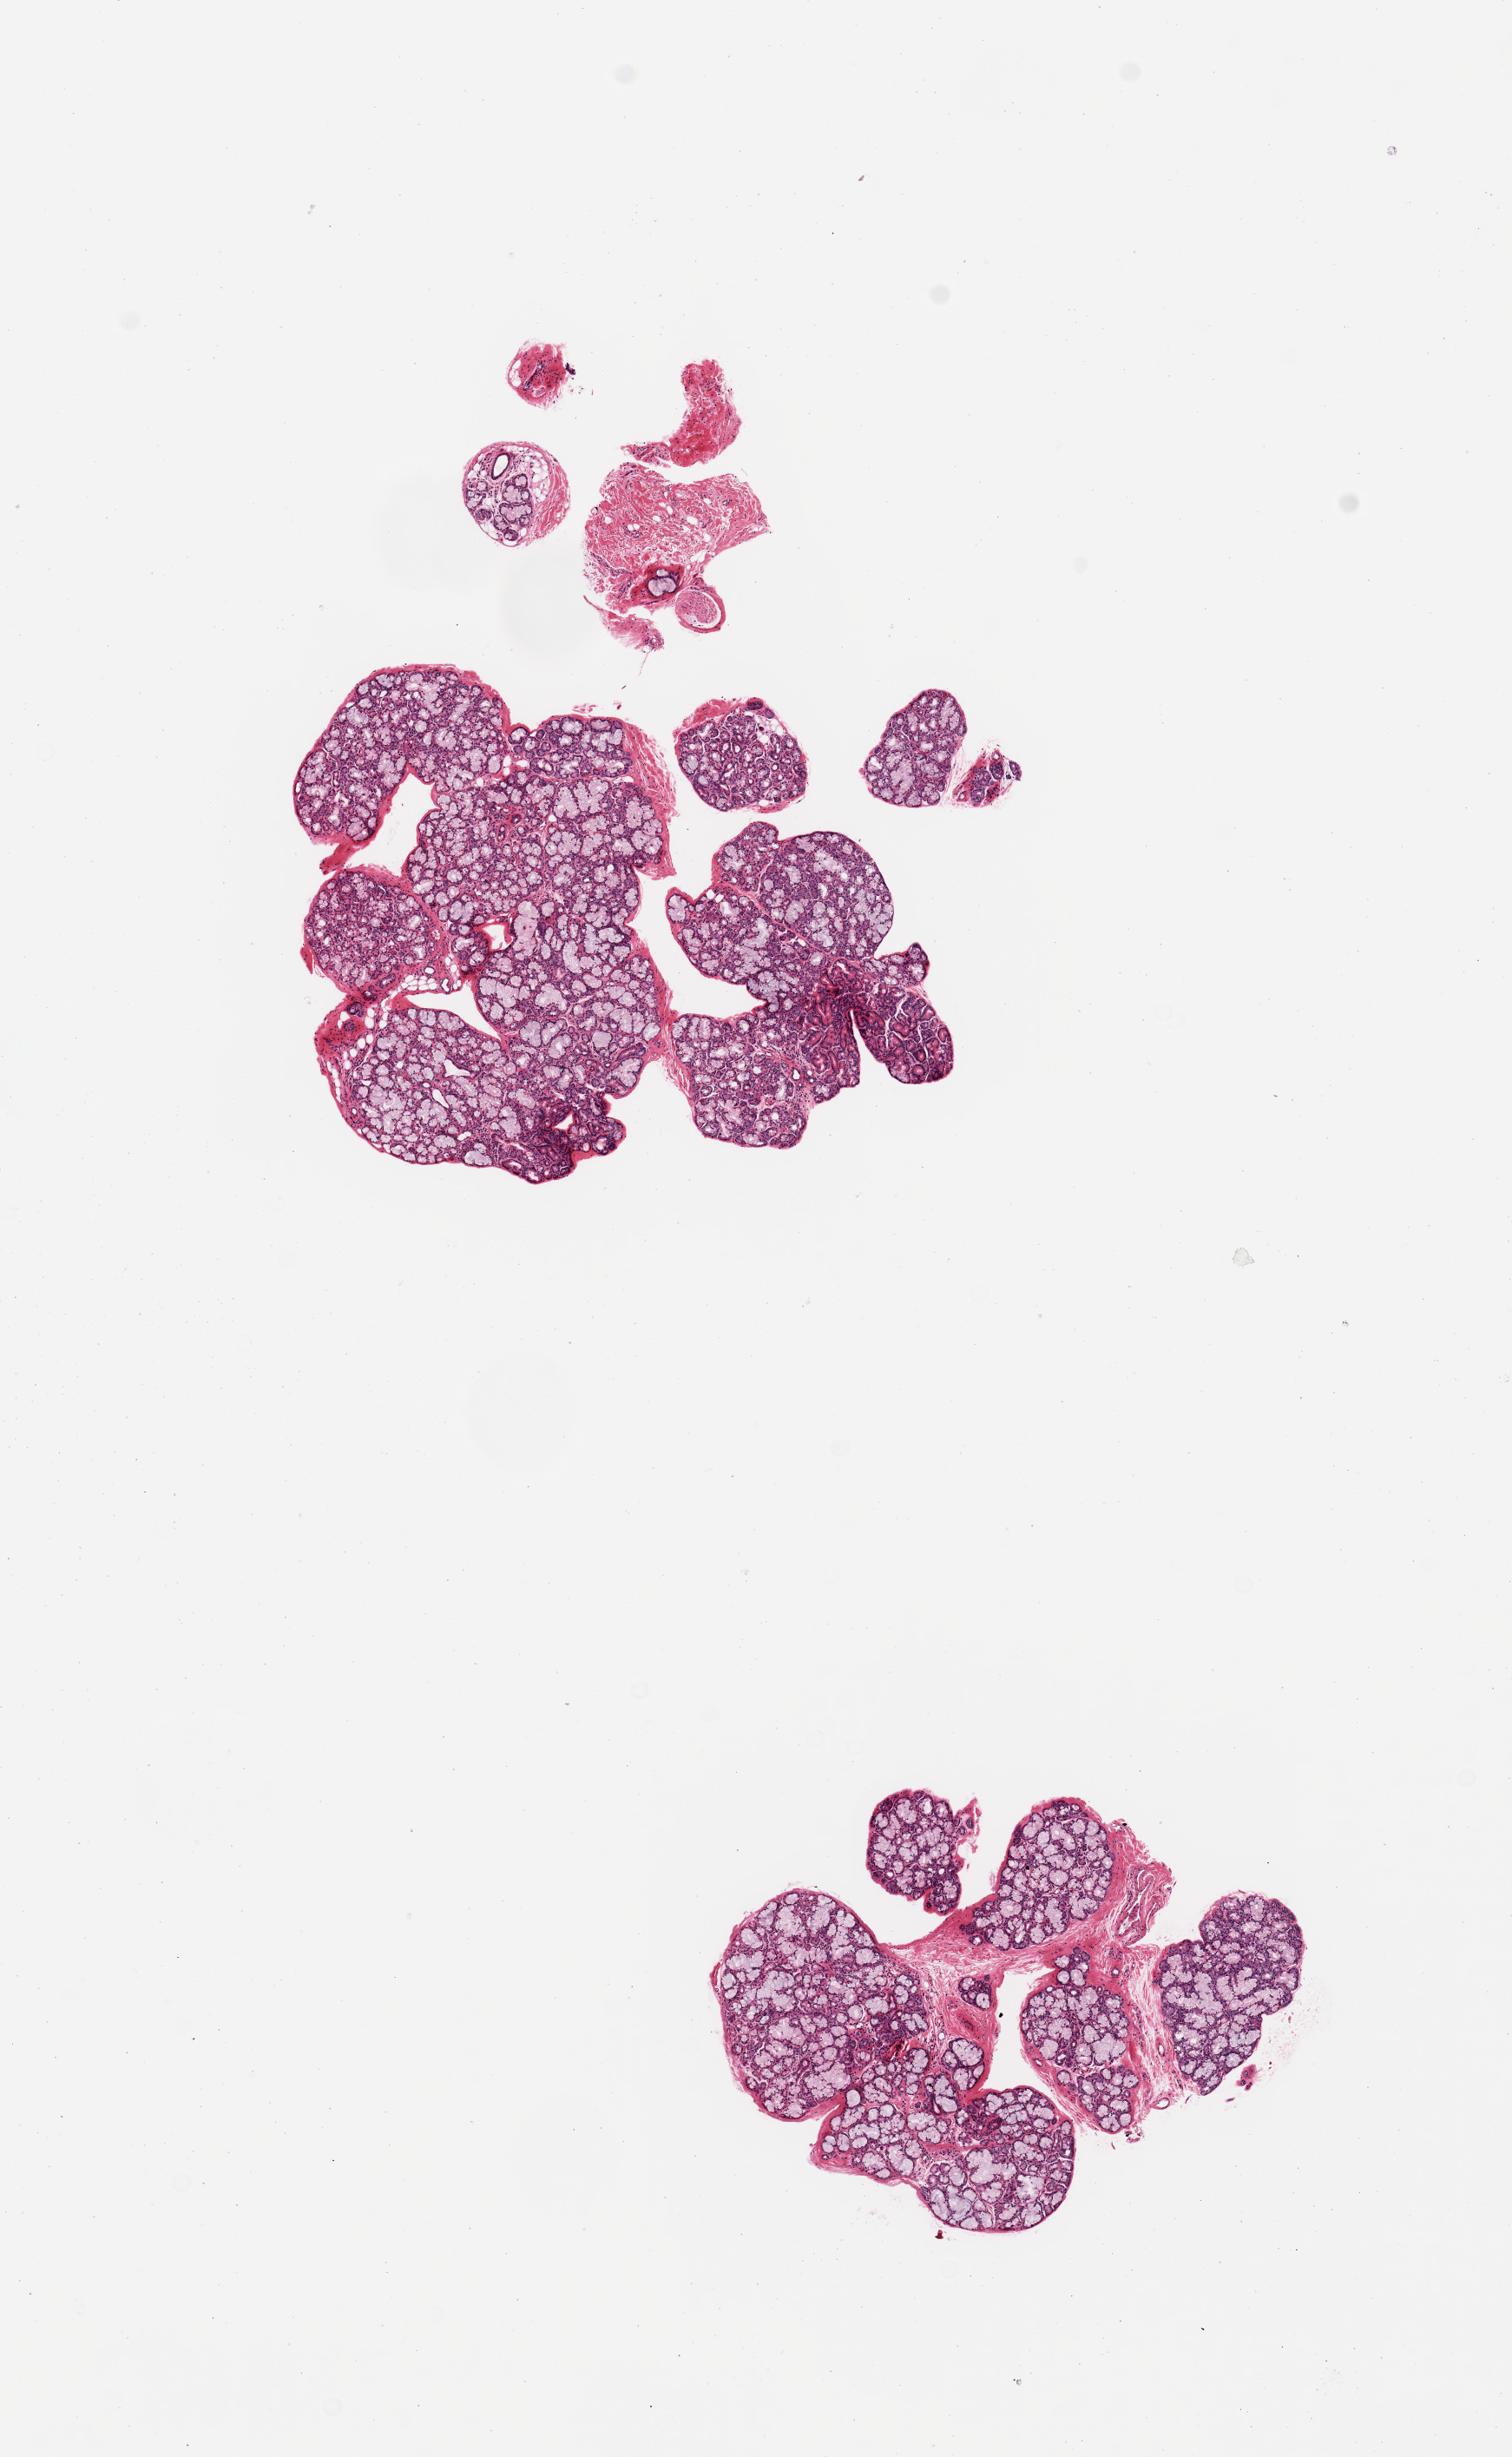
Digitized hematoxylin and eosin (H&E)-stained section, brightfield, whole scanned area (about 6.9 x 11.2 mm) shown as a low-resolution overview; PAXgene-fixed paraffin-embedded (PFPE) section; sampled site (target tissue): minor salivary gland; donor tissue sample. Donor: male.
Pathologist's review note for this sample: 2 pieces; mucous glandular and ductal elements and fragmented fibrovascular tissue with fat and nerves.